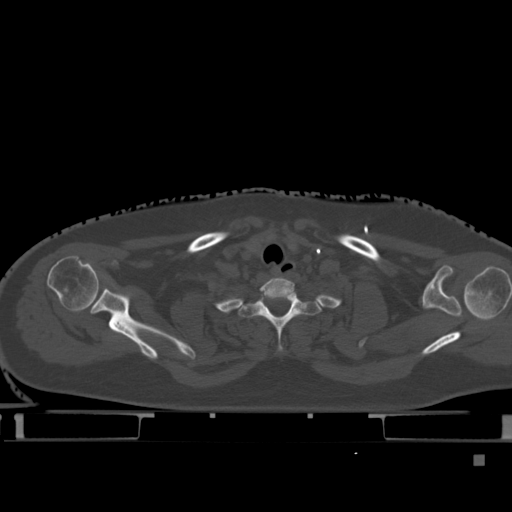
CT including the spine, one axial slice; slice 373 of 495 in the series (ordered by position); bone window (W 1800 / L 400 HU); 1.5 mm slice thickness; 512 × 512 image matrix, field of view 404 × 404 mm. Patient: female, 33 years. From the clinical record (not read from this slice): primary cancer: breast; vertebrae with lytic lesions (as recorded): T1.
Outlined on this slice (semi-automatic segmentation, software-assisted and operator-edited):
- T1 vertebra: bounding box [x1, y1, x2, y2] px = [239, 289, 322, 353]